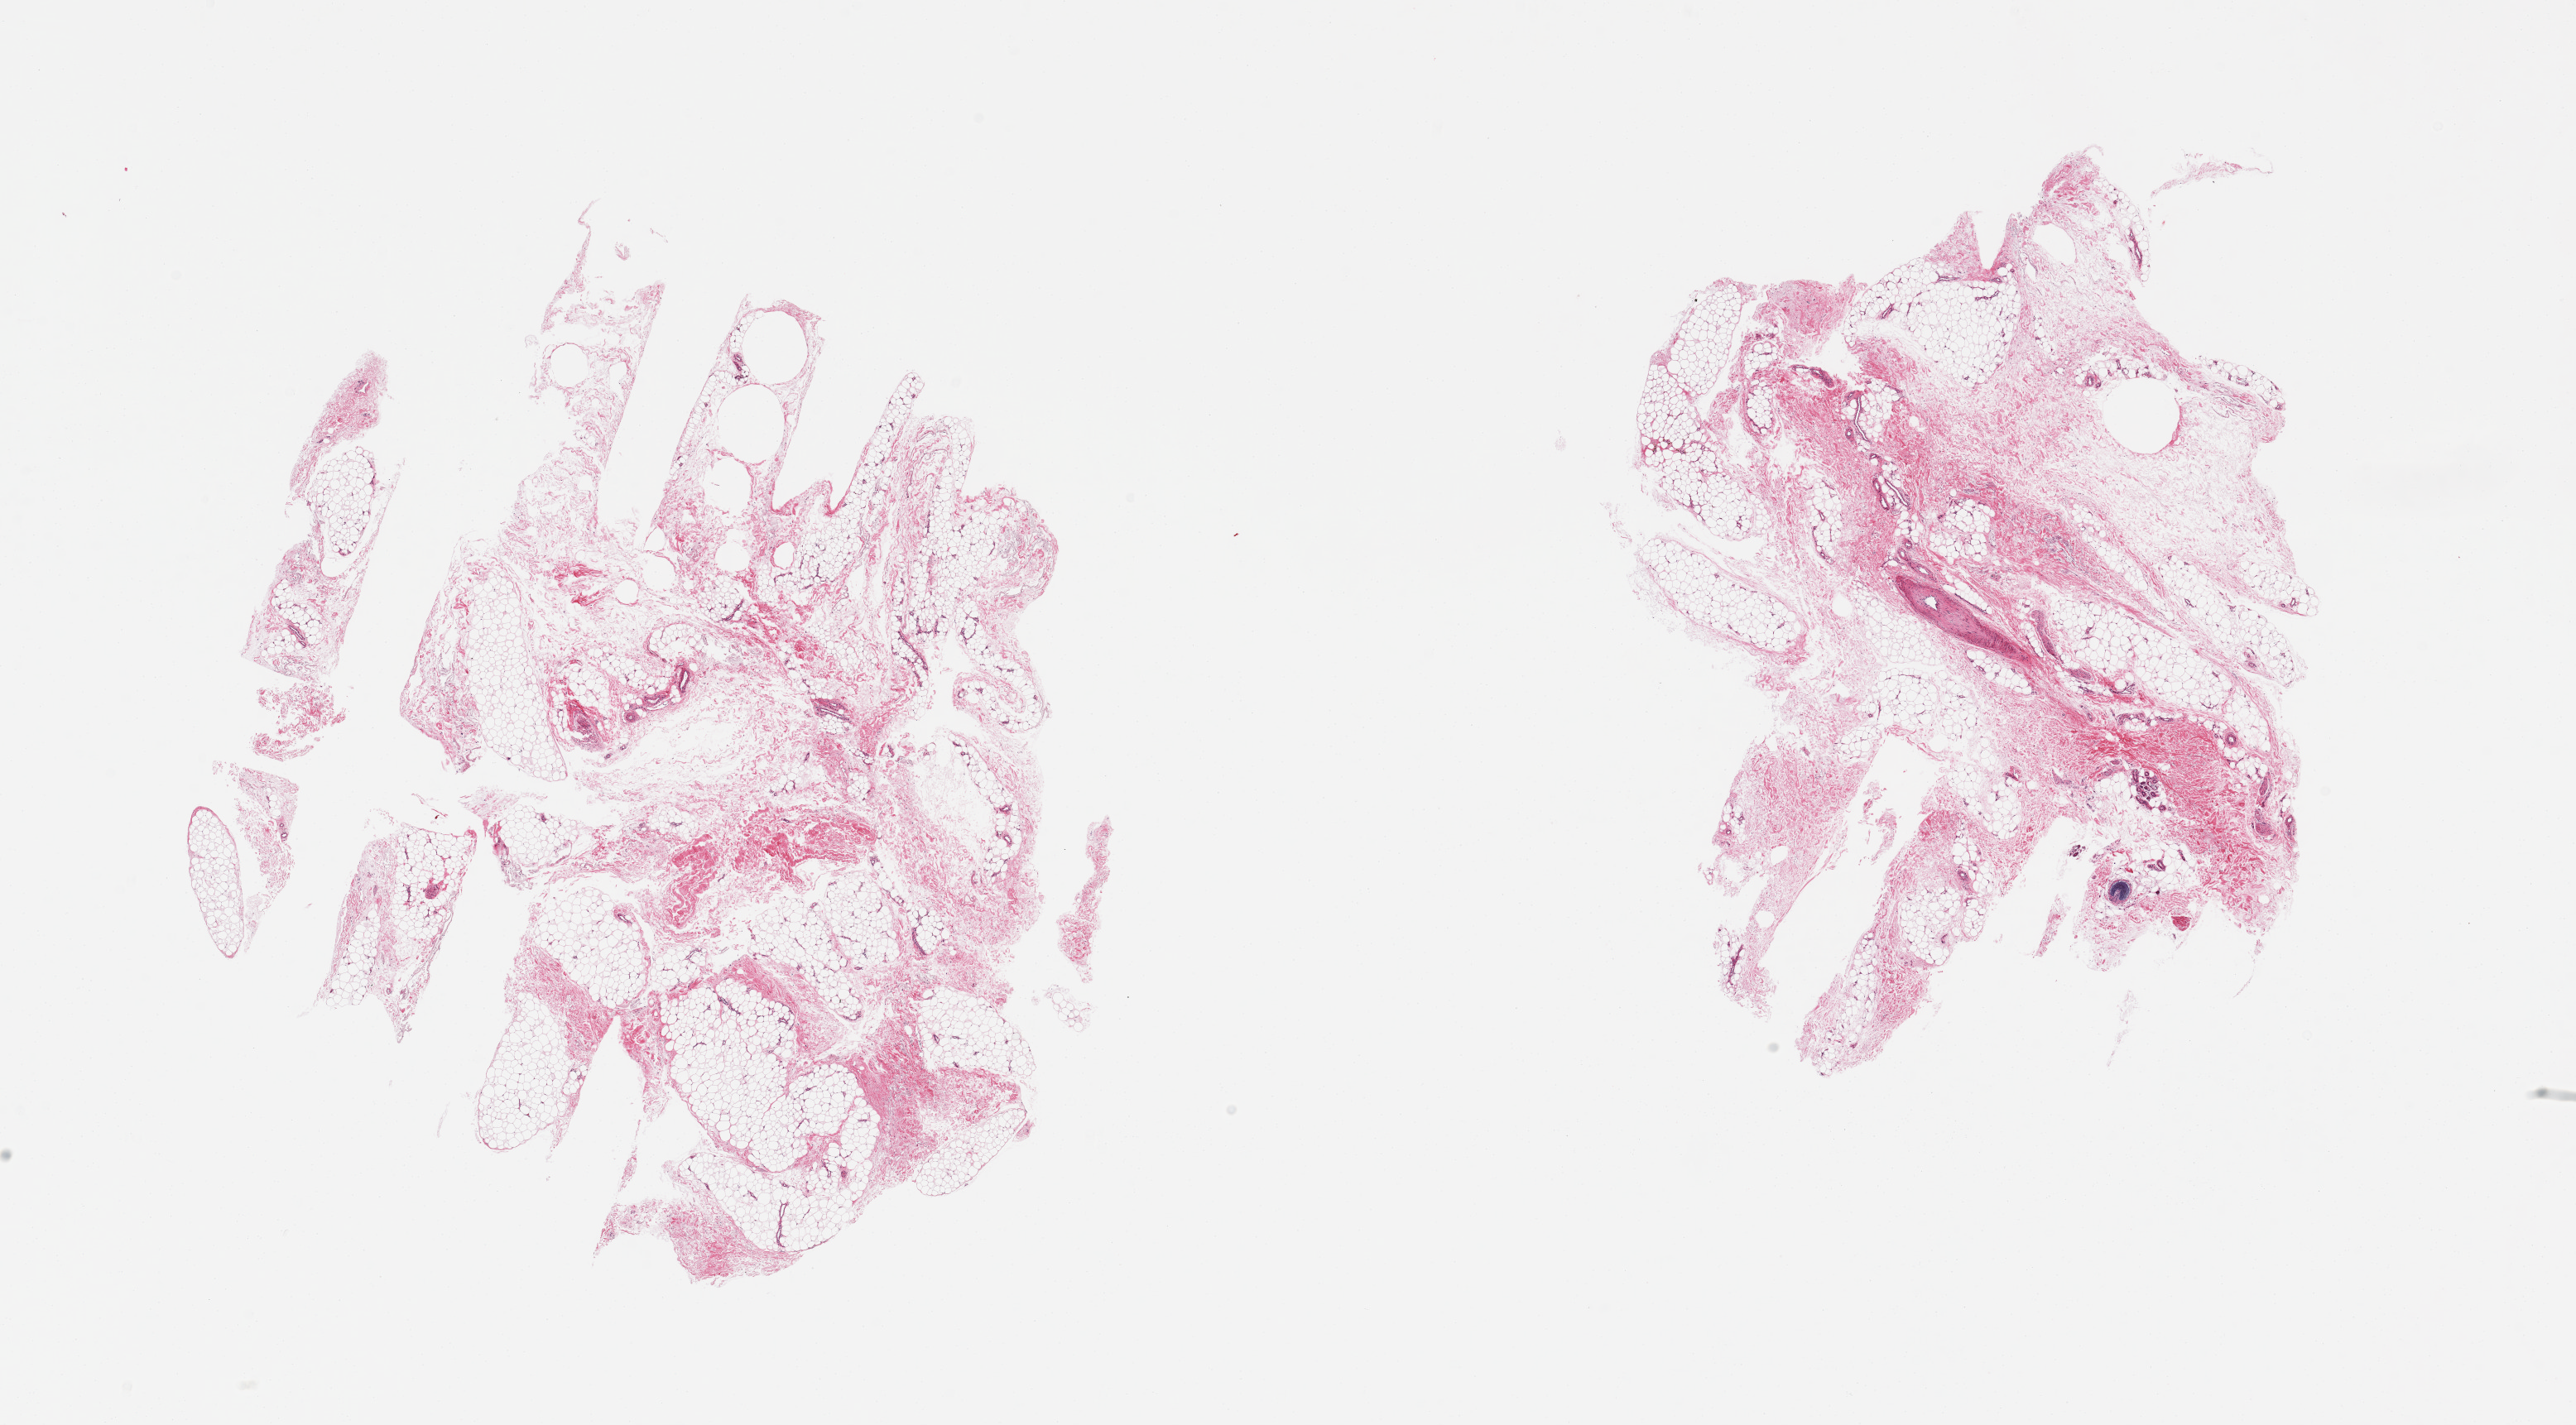
Whole-slide image, hematoxylin and eosin (H&E) stain, a low-resolution overview of the entire scanned area, about 24.6 x 13.6 mm, PAXgene-fixed paraffin-embedded (PFPE) section, target tissue: adipose tissue, tissue donor sample. Donor sex: male.
• review note (as recorded): 2 pieces; mature adipose tissue with fibrovascular component; one contains hair bulb, adnexa, nerves and vessels